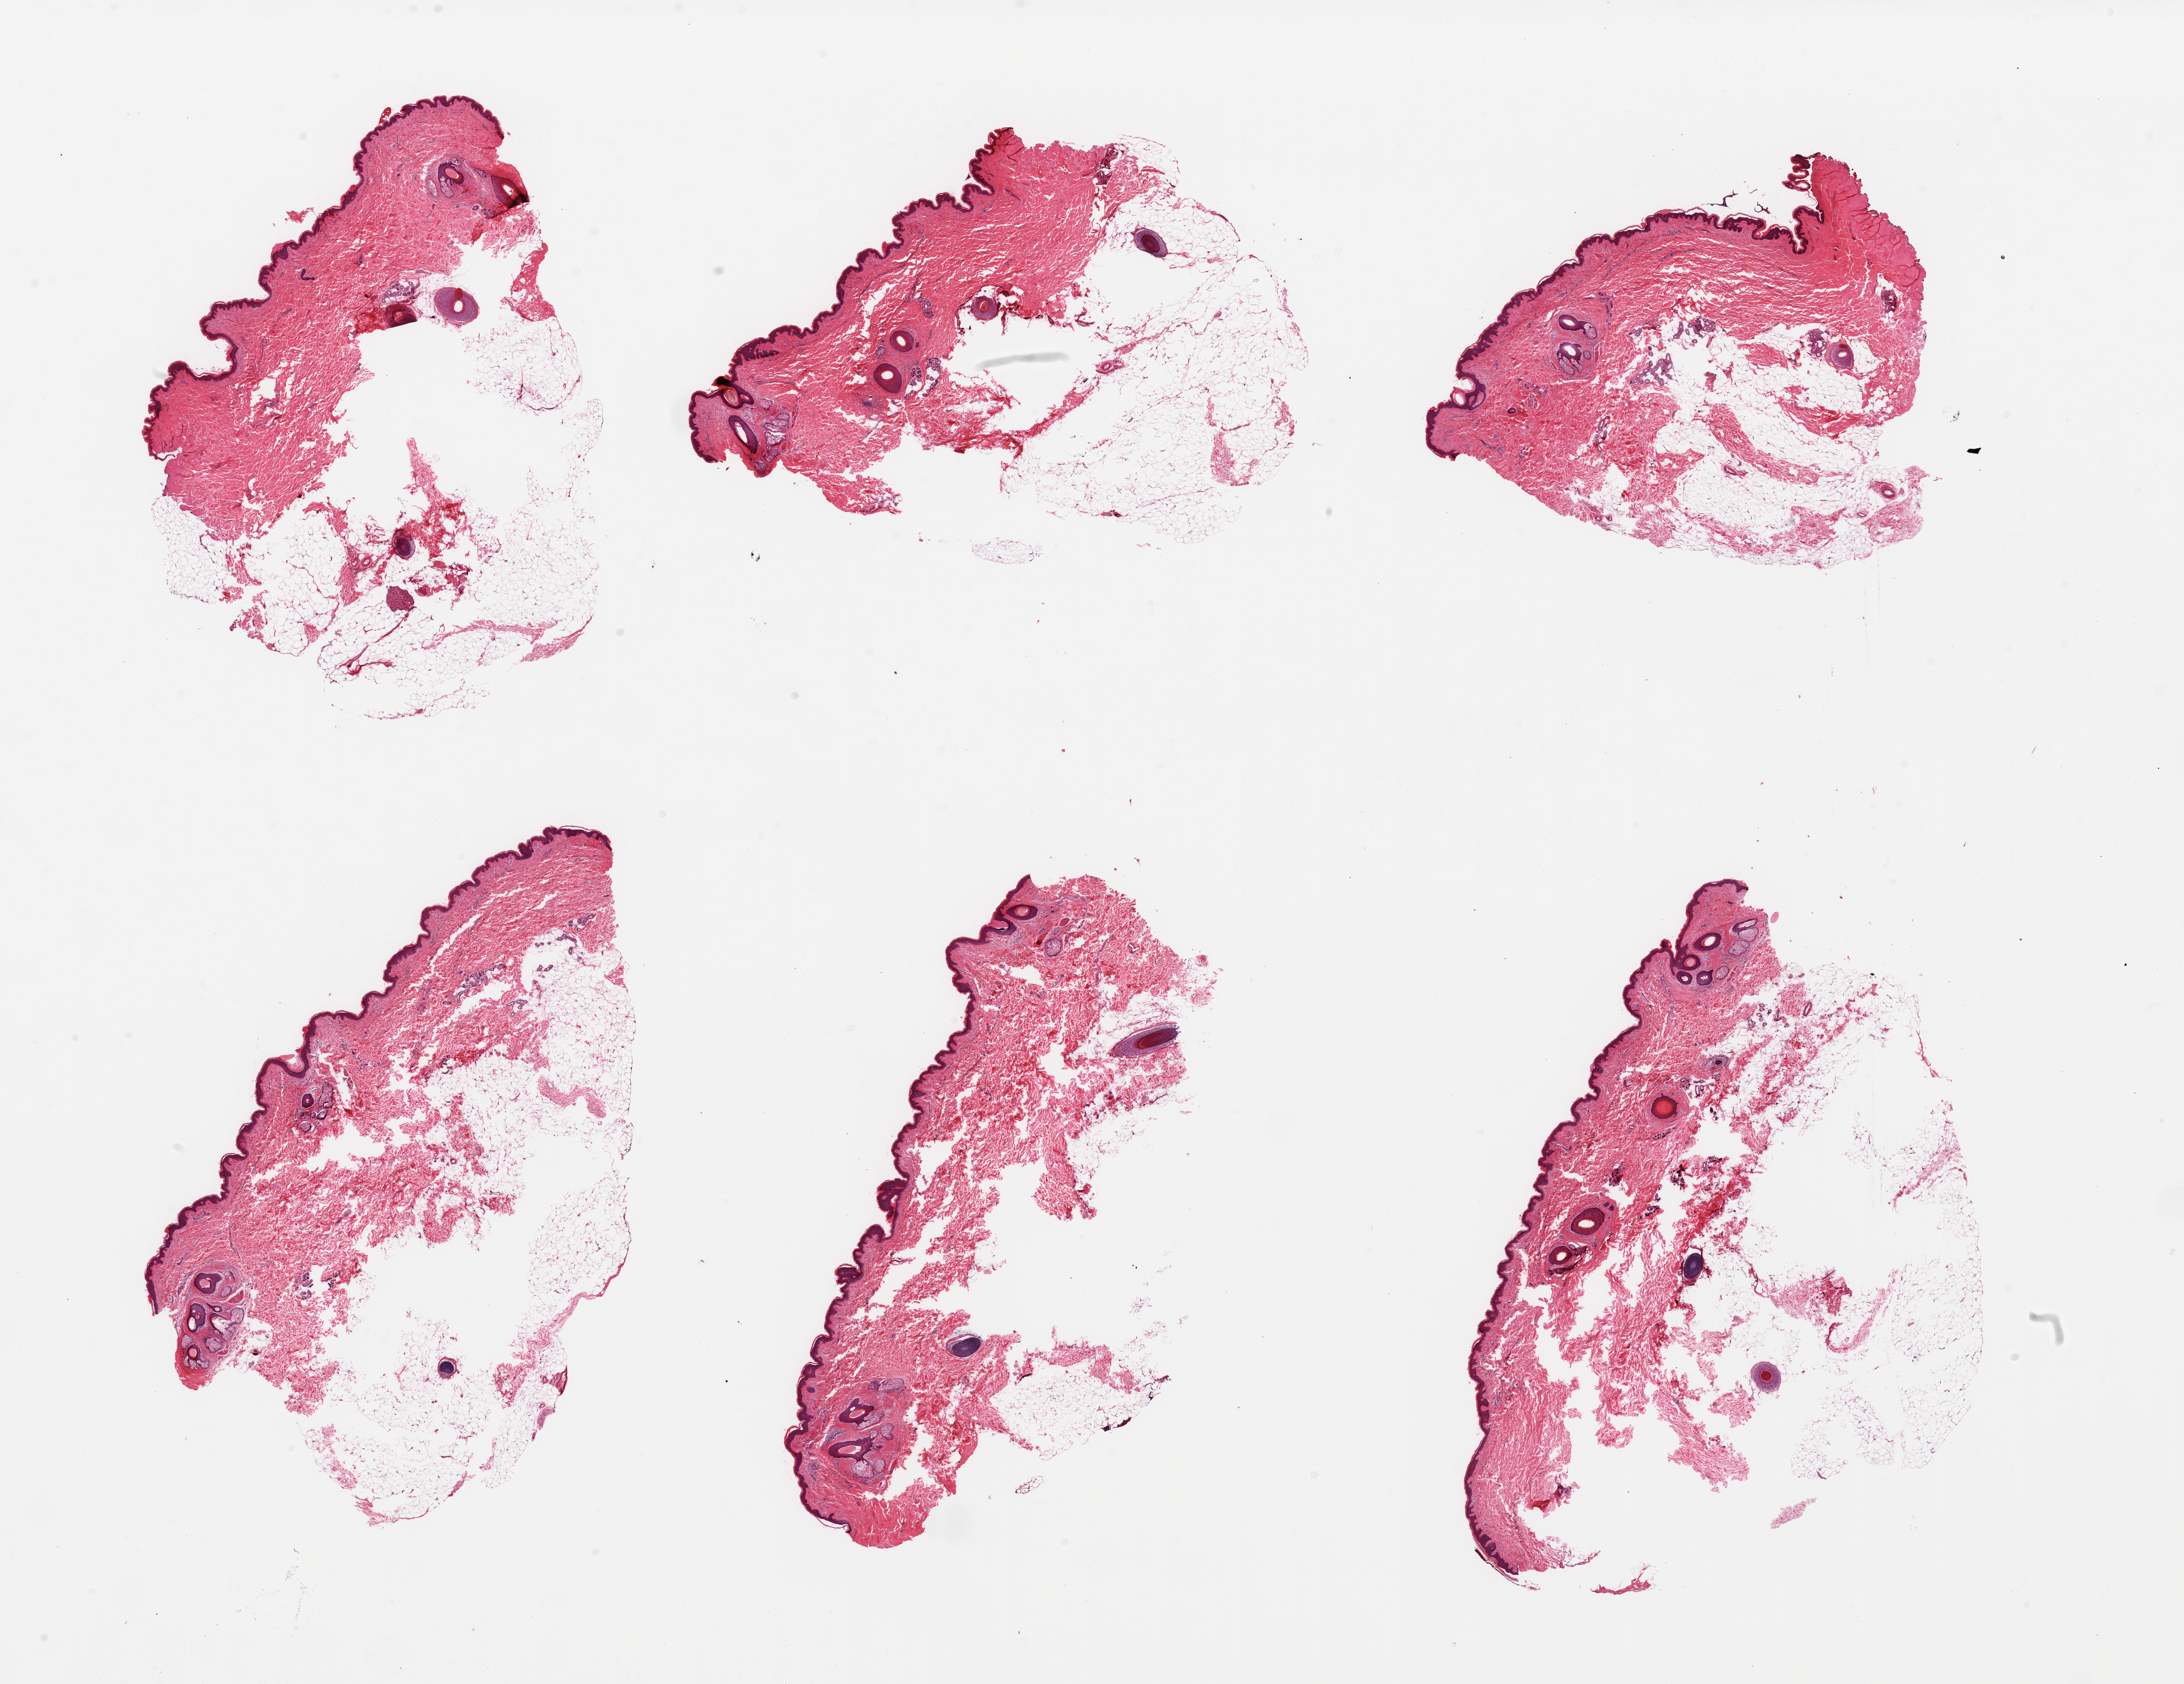
Digitized H&E-stained section — whole scanned area (about 27.6 x 21.3 mm) shown as a low-resolution overview. PAXgene-fixed paraffin-embedded (PFPE) section. Target tissue: skin of suprapubic region. Donor tissue sample. Male donor.
Reviewer comment on this tissue sample: 6 pieces, squamous epithelium is ~50-60 microns, abundant dermal fat up to ~2.8mm.